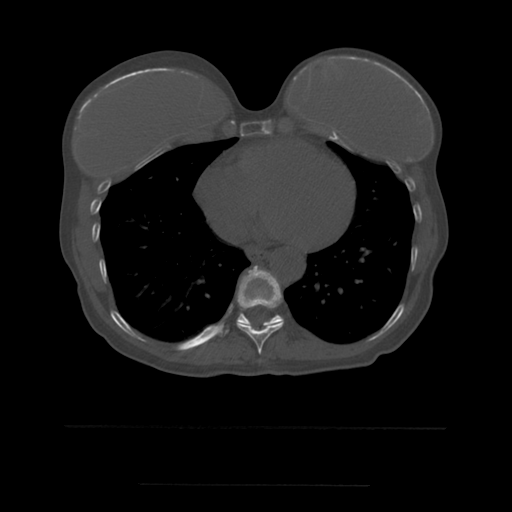
CT including the spine, one axial slice; slice 314 of 544 in the series (ordered by position); bone window (W 1800 / L 400 HU); 1.25 mm slice thickness; 512 × 512 image matrix. Patient age 58 years. Case-level facts recorded for this patient, not image findings: primary cancer: lung.
Outlined on this slice (semi-automatic segmentation, software-assisted and operator-edited):
- T10 vertebra: bounding box <216,313,283,336> (left, top, right, bottom; pixels)
- T9 vertebra: <236,266,284,354>